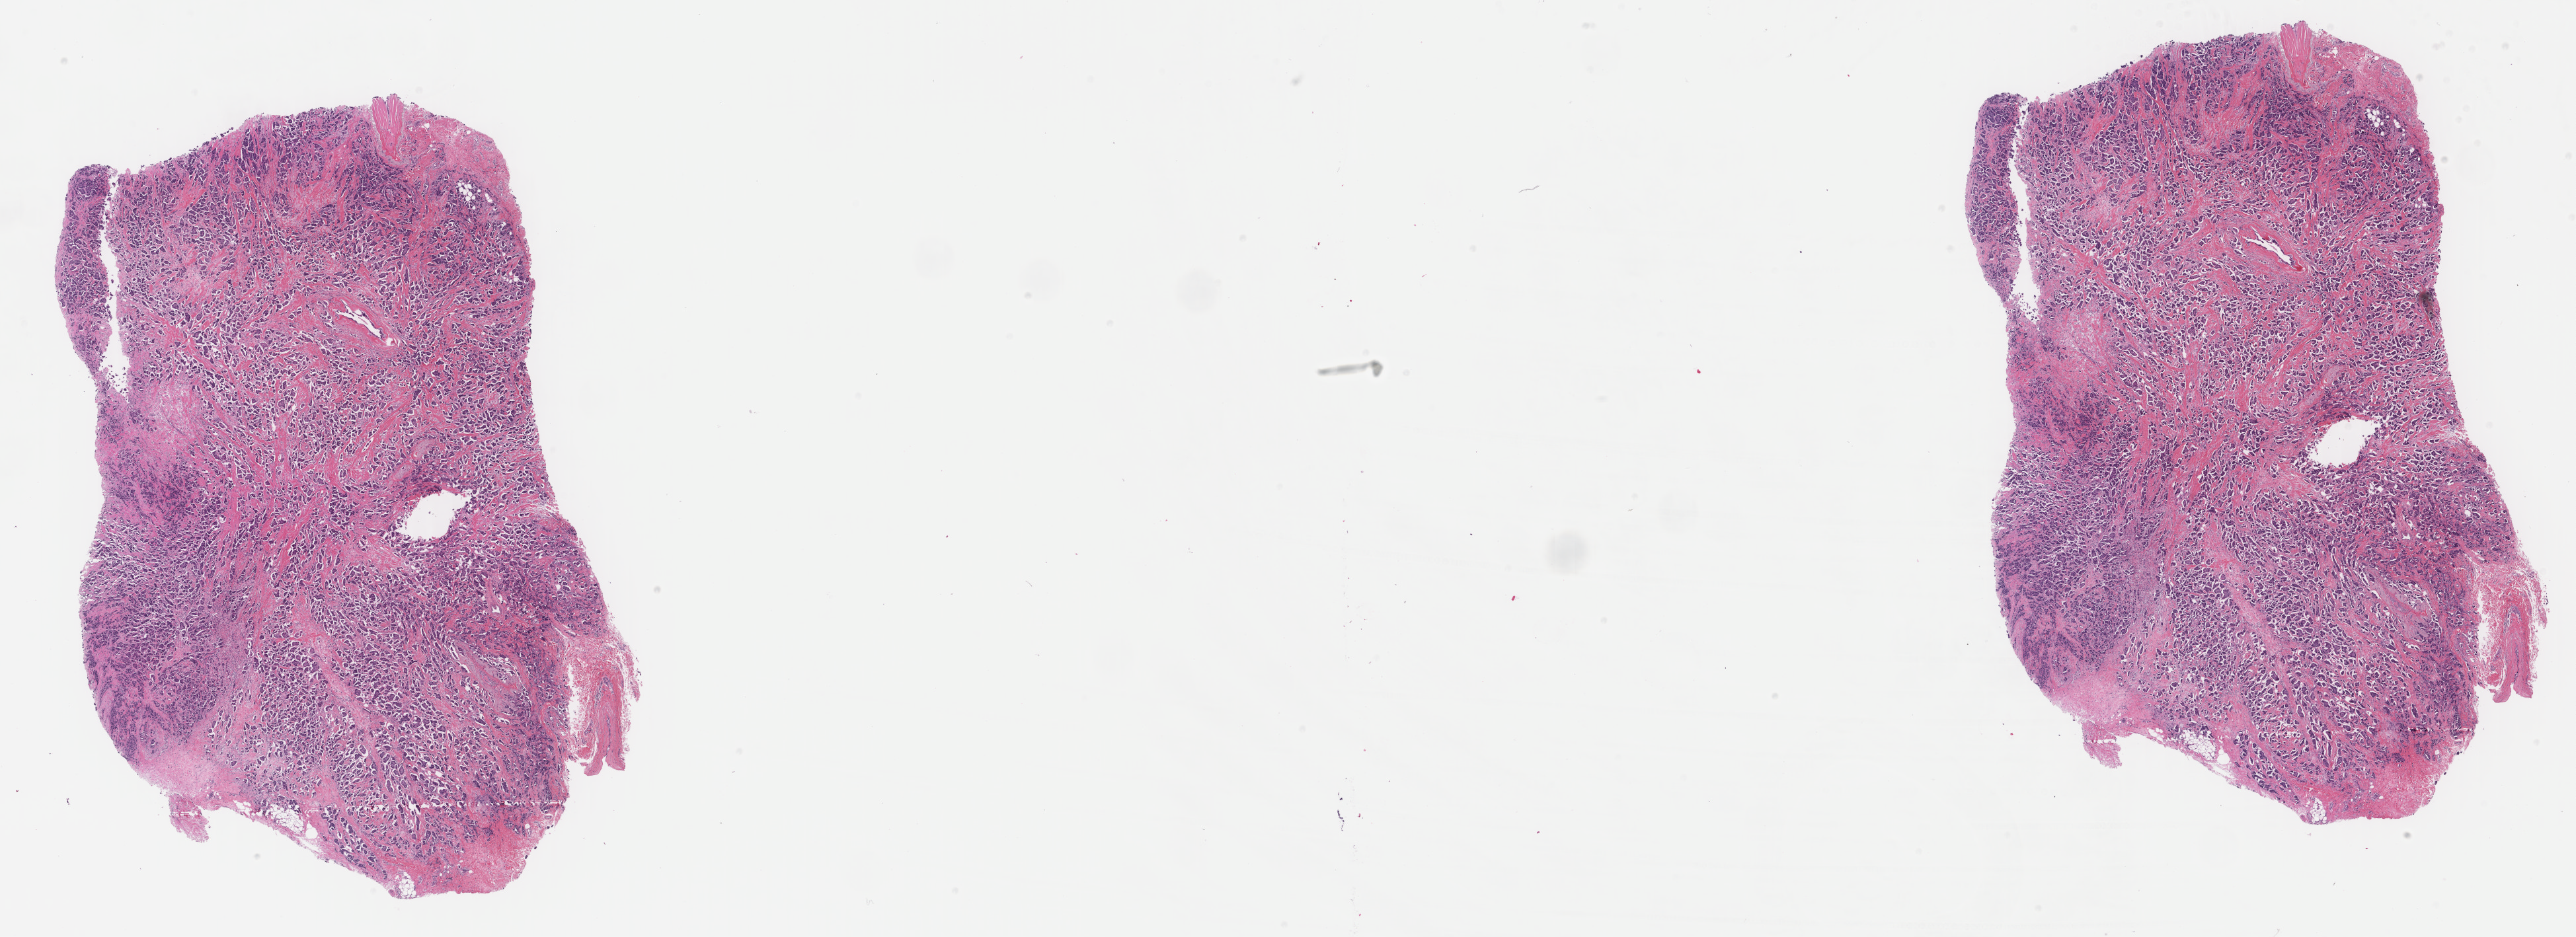
H&E whole-slide image — whole scanned area (about 30.9 x 11.3 mm, from a 40x scan) shown as a low-resolution overview. FFPE section. Breast, primary tumour sample. Patient: female, age at initial diagnosis 63 years.
Histologic diagnosis: Infiltrating duct carcinoma, NOS.